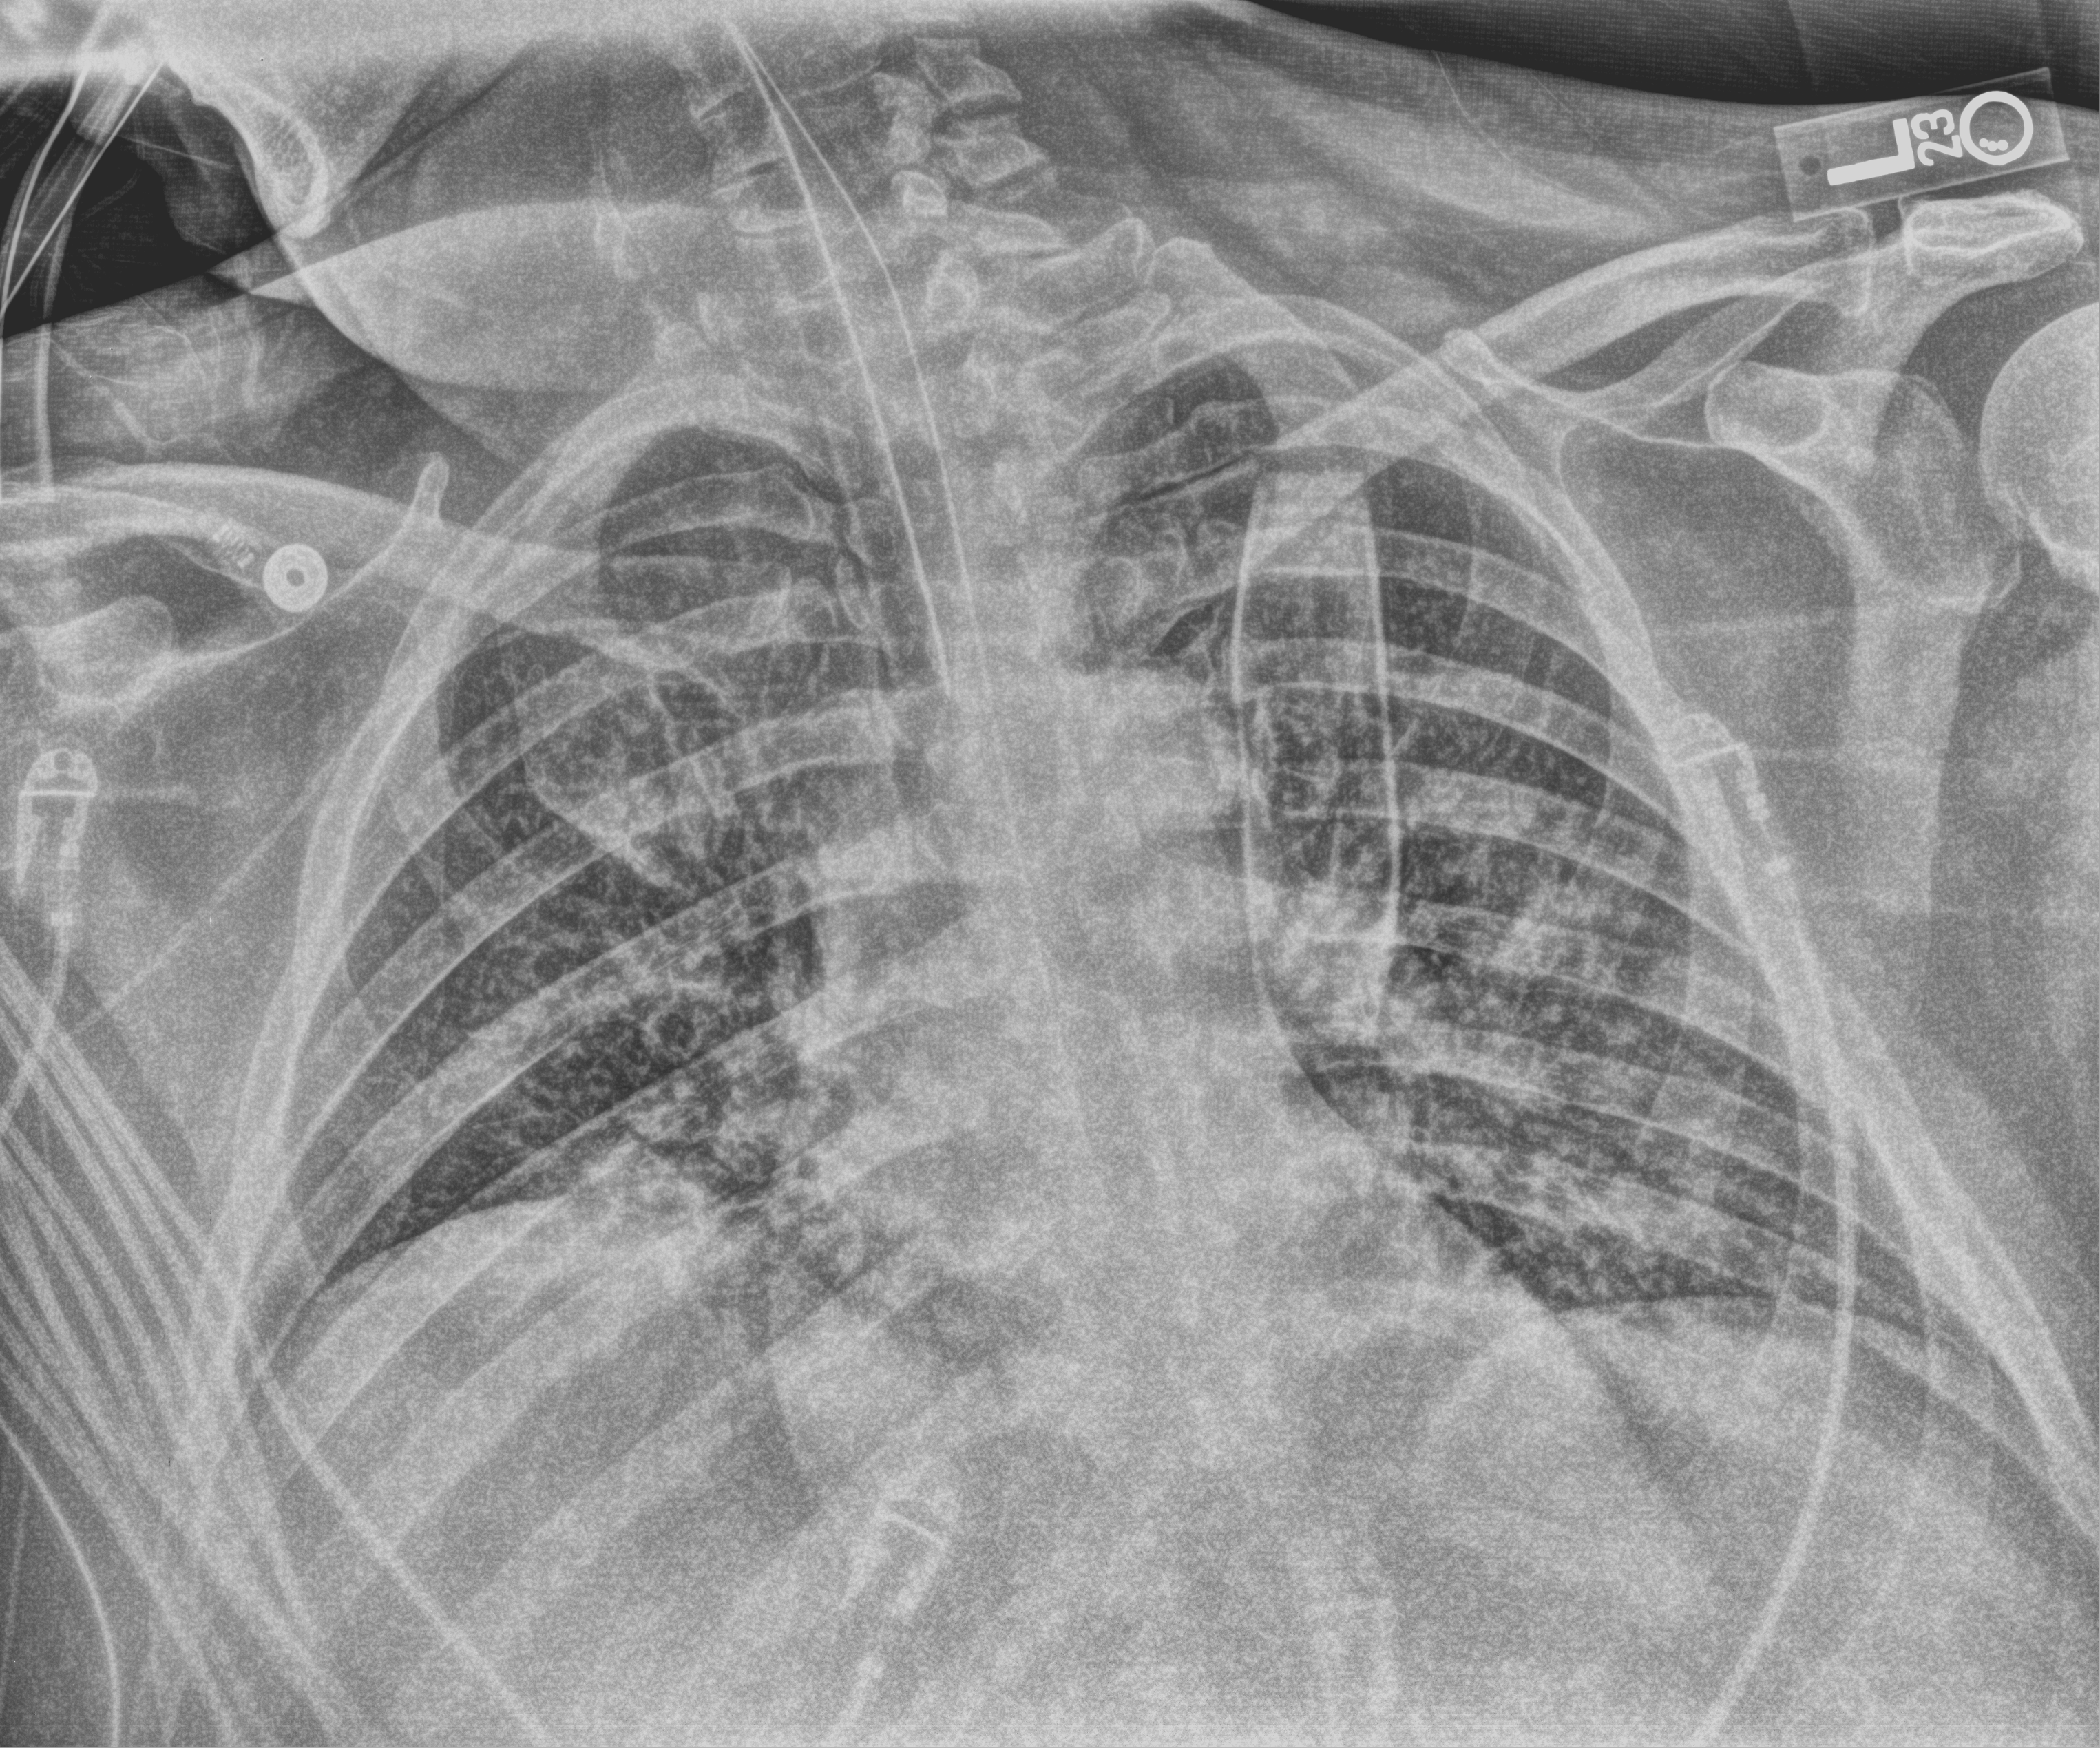
Portable chest radiograph, anteroposterior (AP) projection. Patient hospitalised with COVID-19; male, aged 18–59 years.
Admission-level facts for this patient (not findings on this image; timing relative to this image not recorded):
- smoking status (admission record): never
- diabetes (admission record): yes